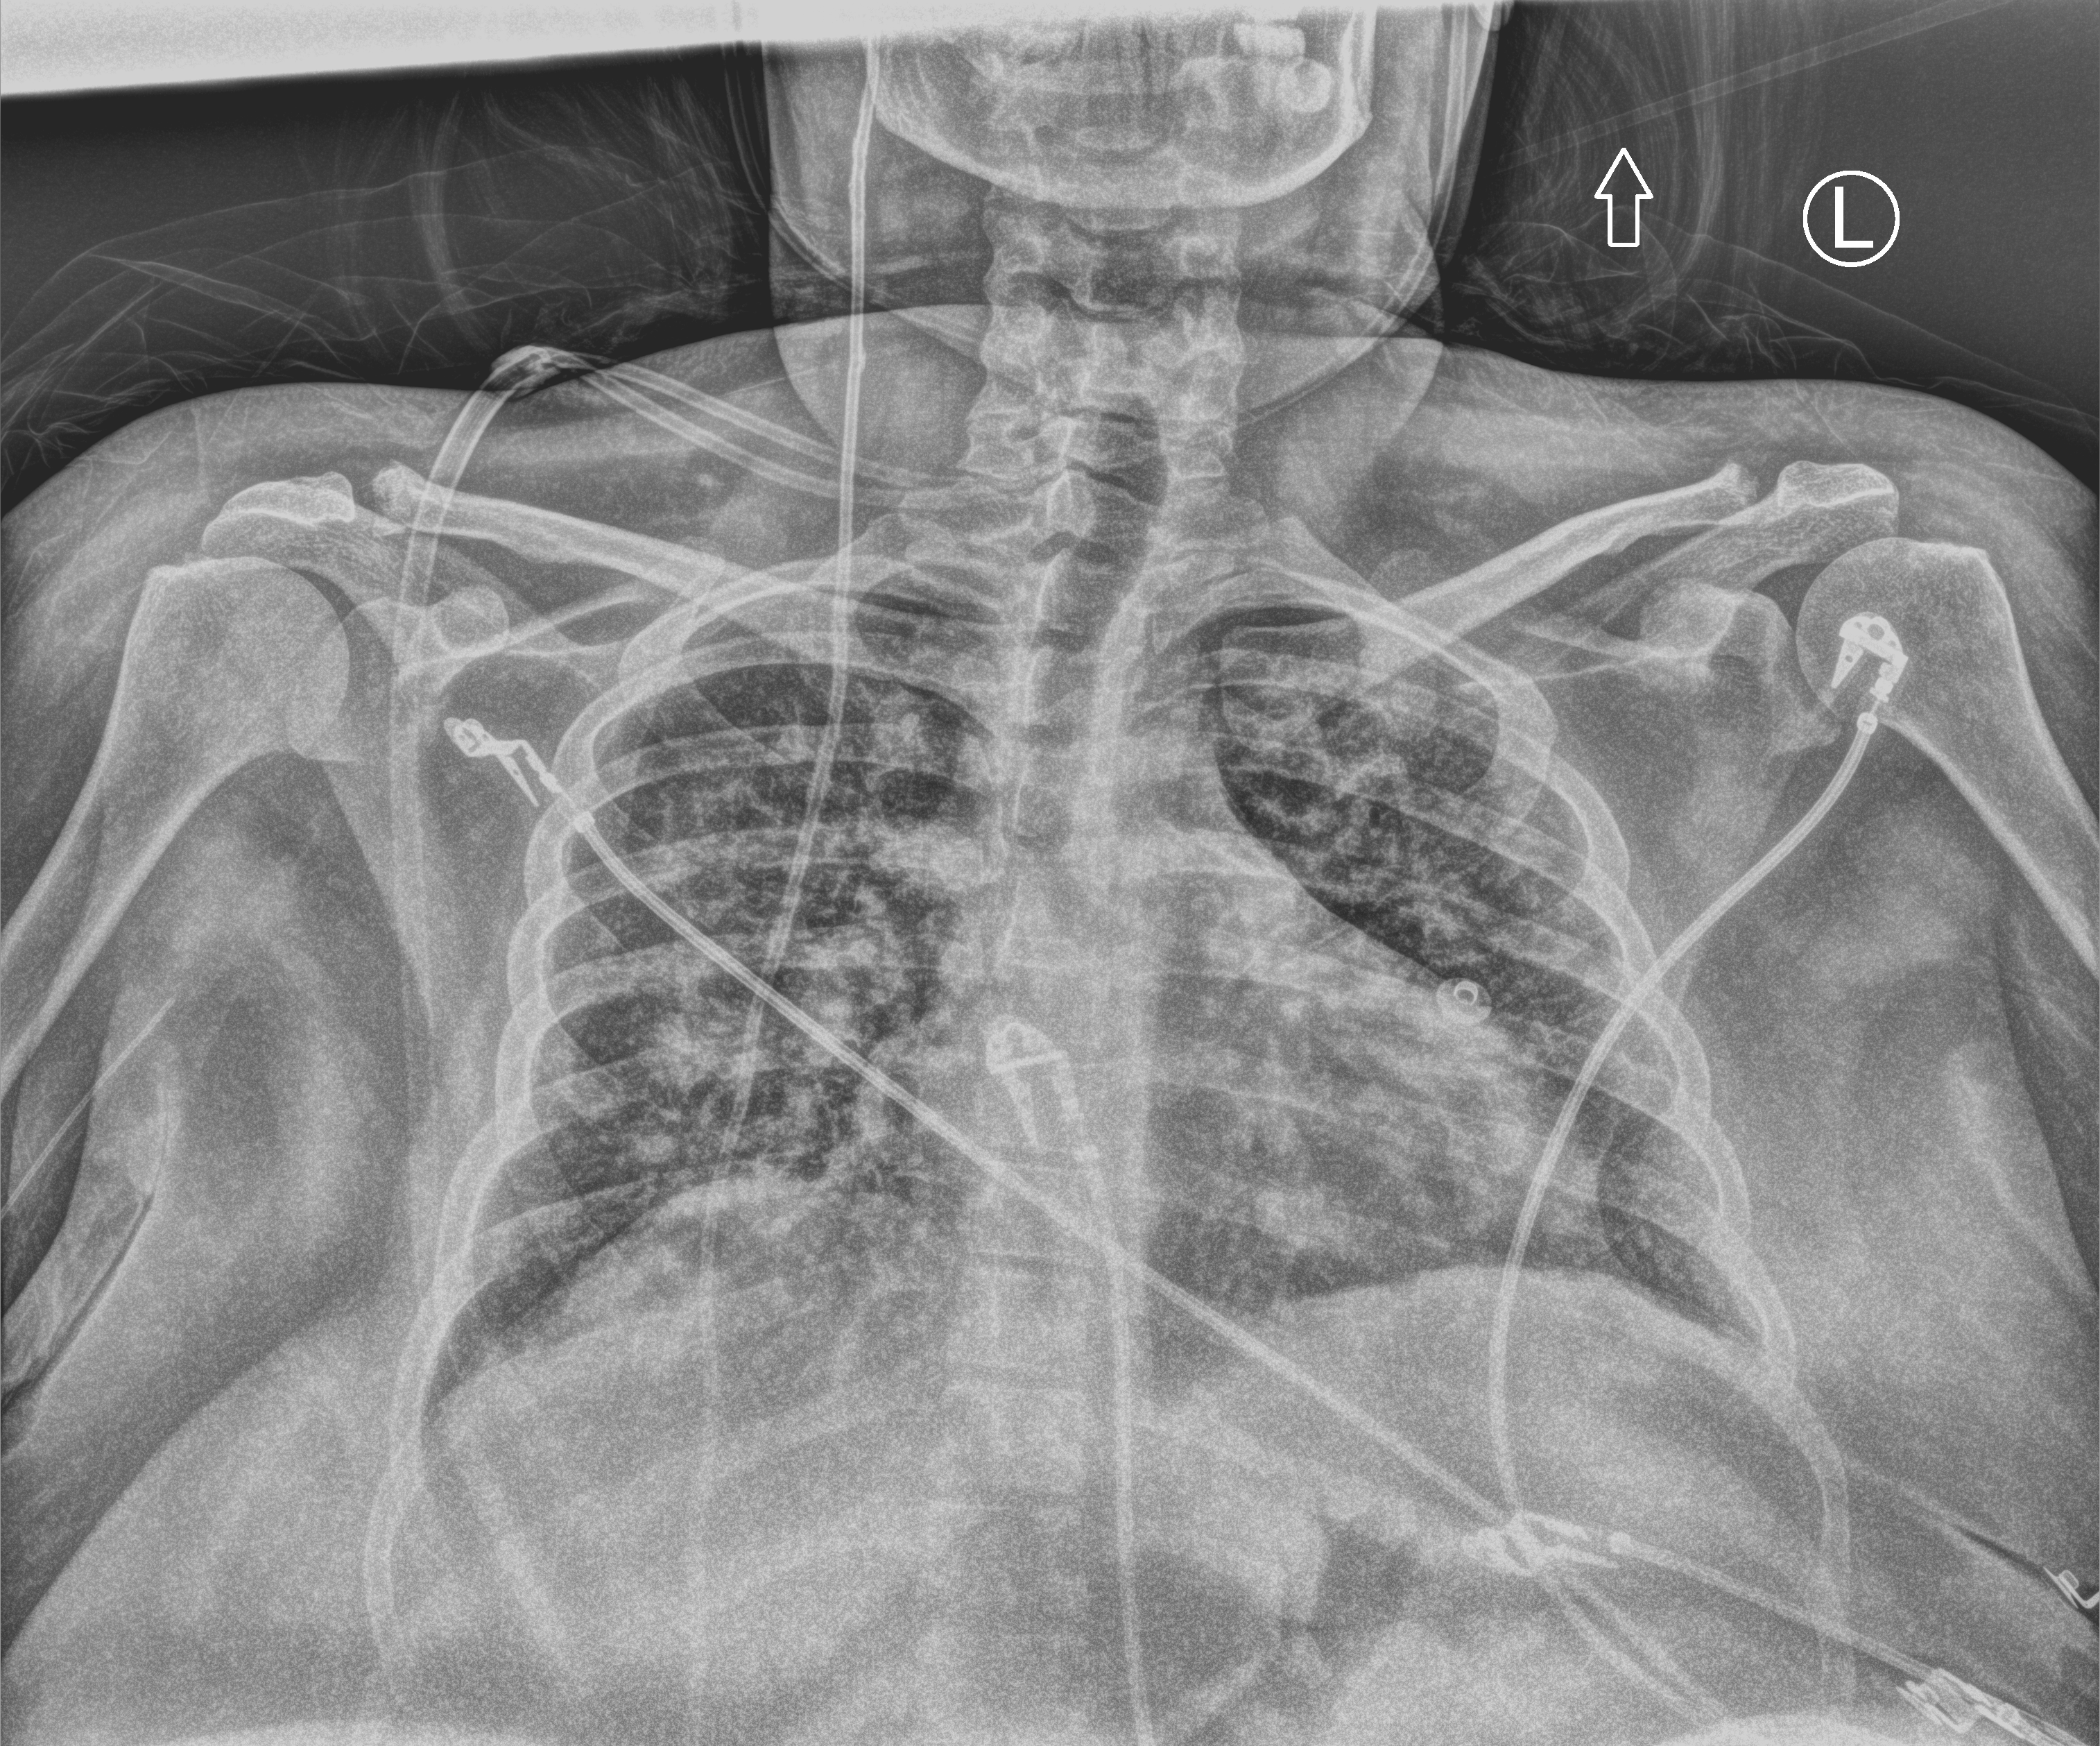
Bedside chest radiograph (computed radiography). Female patient hospitalised with COVID-19, age 18–59 years.
From the hospital-stay record, not from the radiograph (when in the stay this image was taken is not recorded):
- mechanically ventilated during this hospital stay: no